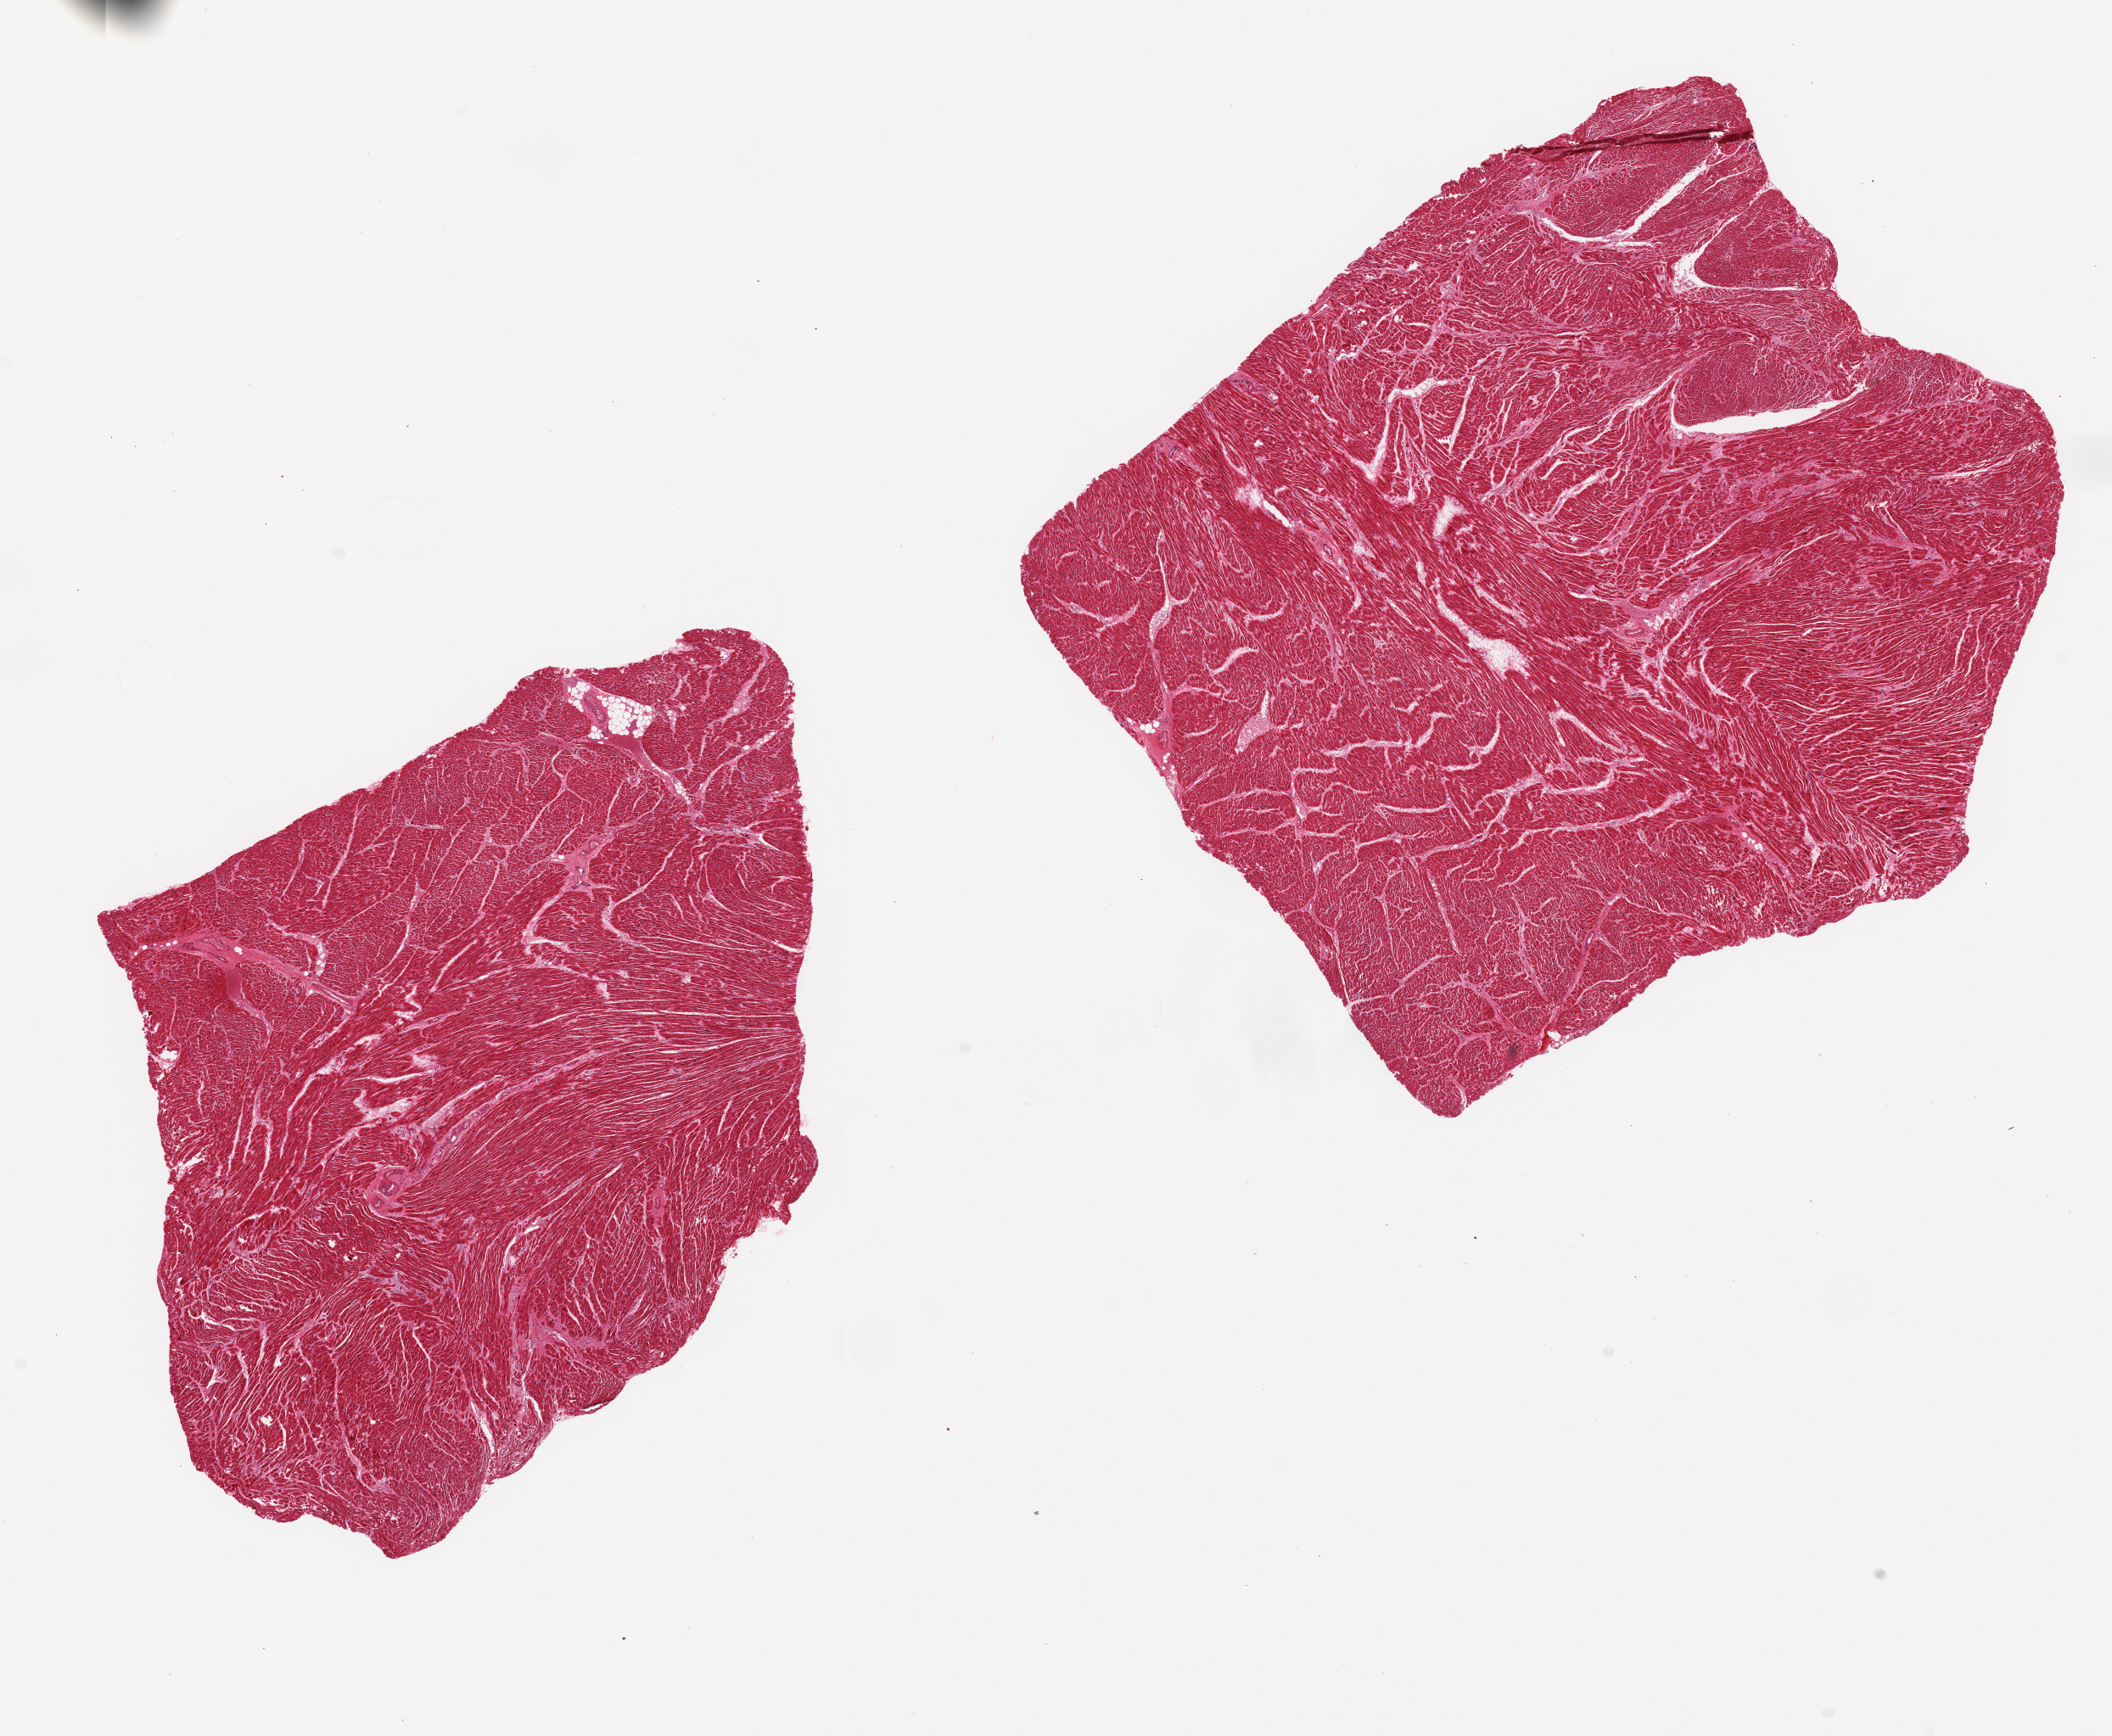
Whole-slide image, haematoxylin and eosin stain, shown as a low-resolution overview of the whole scanned area (about 19.7 x 16.2 mm). PAXgene-fixed paraffin-embedded (PFPE) section. Sampled site (target tissue): heart. Tissue donor sample. Donor: female.
Review note (as recorded): 2 pieces ~7x7mm, focal insterstitial fibrosis; Unusually poorly preserved.